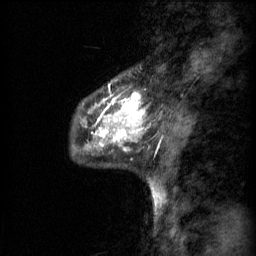
Breast MRI (dynamic contrast-enhanced), one sagittal slice; slice 19 of 60 in the series (ordered by position); 3 images stored at this slice position (order not interpretable as contrast timing); 1.5 T; TE 4.2 ms, TR 11 ms; 2 mm slice thickness; 256 × 256 image matrix, field of view 200 × 200 mm. Patient: female, 48 years.
Structures marked on this image (semi-automatic segmentation, software-assisted and operator-edited):
- analysis volume of interest (the breast-tissue region the enhancement analysis was run in; not a lesion): bounding box (x1, y1, x2, y2) in pixels: (77, 80, 150, 147)
- tumour enhancement mask (voxels above the 70 % enhancement threshold inside the analysis volume of interest): (95, 84, 145, 147)